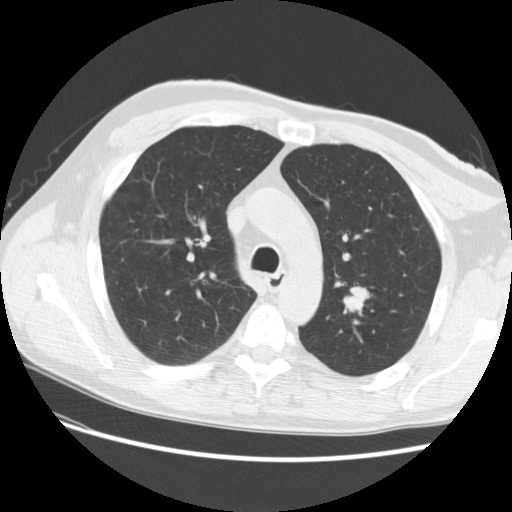
Low-dose screening chest CT, one axial slice; position 184 of 256 along the scan axis; 120 kVp; lung window (W 1500 / L -600 HU); 2.5 mm slice thickness; 512 × 512 image matrix, field of view 366 × 366 mm.
Annotated regions visible in this slice (expert manual segmentation):
- lesion 1 (tumor, upper lobe of left lung): bounding box (x1, y1, x2, y2) in pixels: (344, 288, 368, 311)